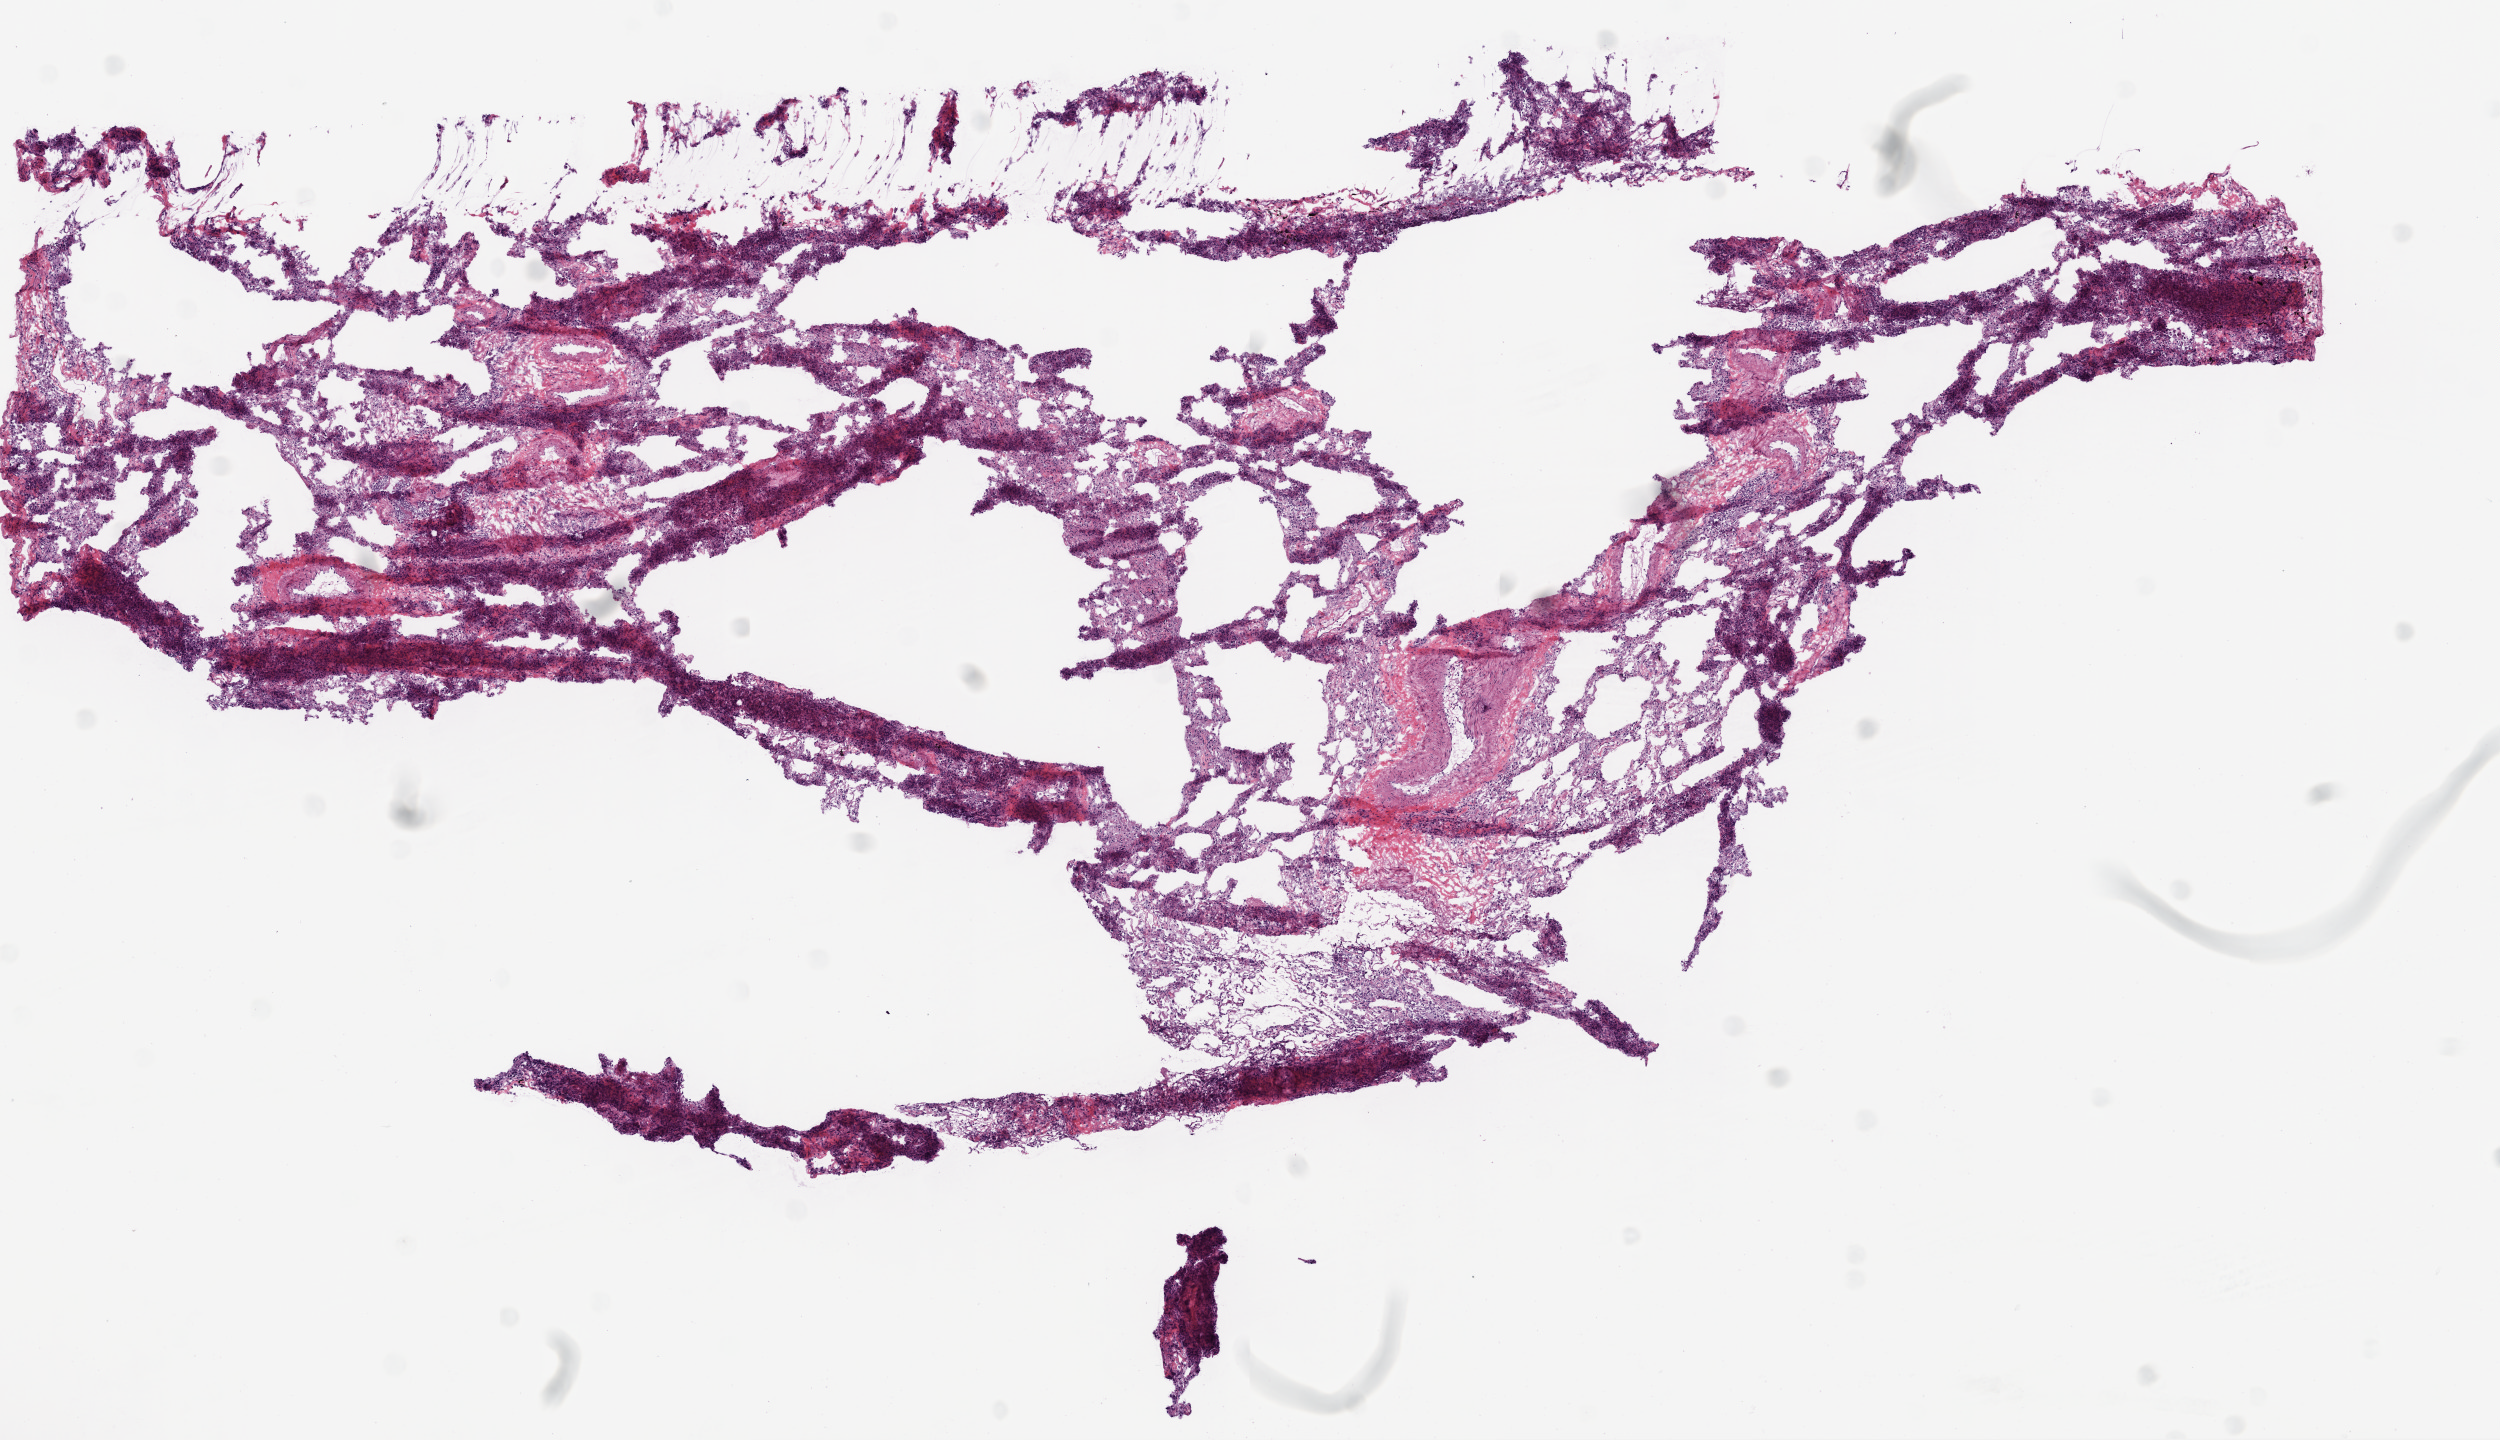
H&E whole-slide image — shown as a low-resolution overview of the whole scanned area (about 10.0 x 5.8 mm). Frozen section from the bottom of the tissue portion. Lung, solid tissue normal (non-tumour tissue) sample. Male, age 68 years at initial diagnosis.
This section: solid tissue normal sample (biorepository sample class). Patient diagnosis: Squamous cell carcinoma, NOS (upper lobe, lung).